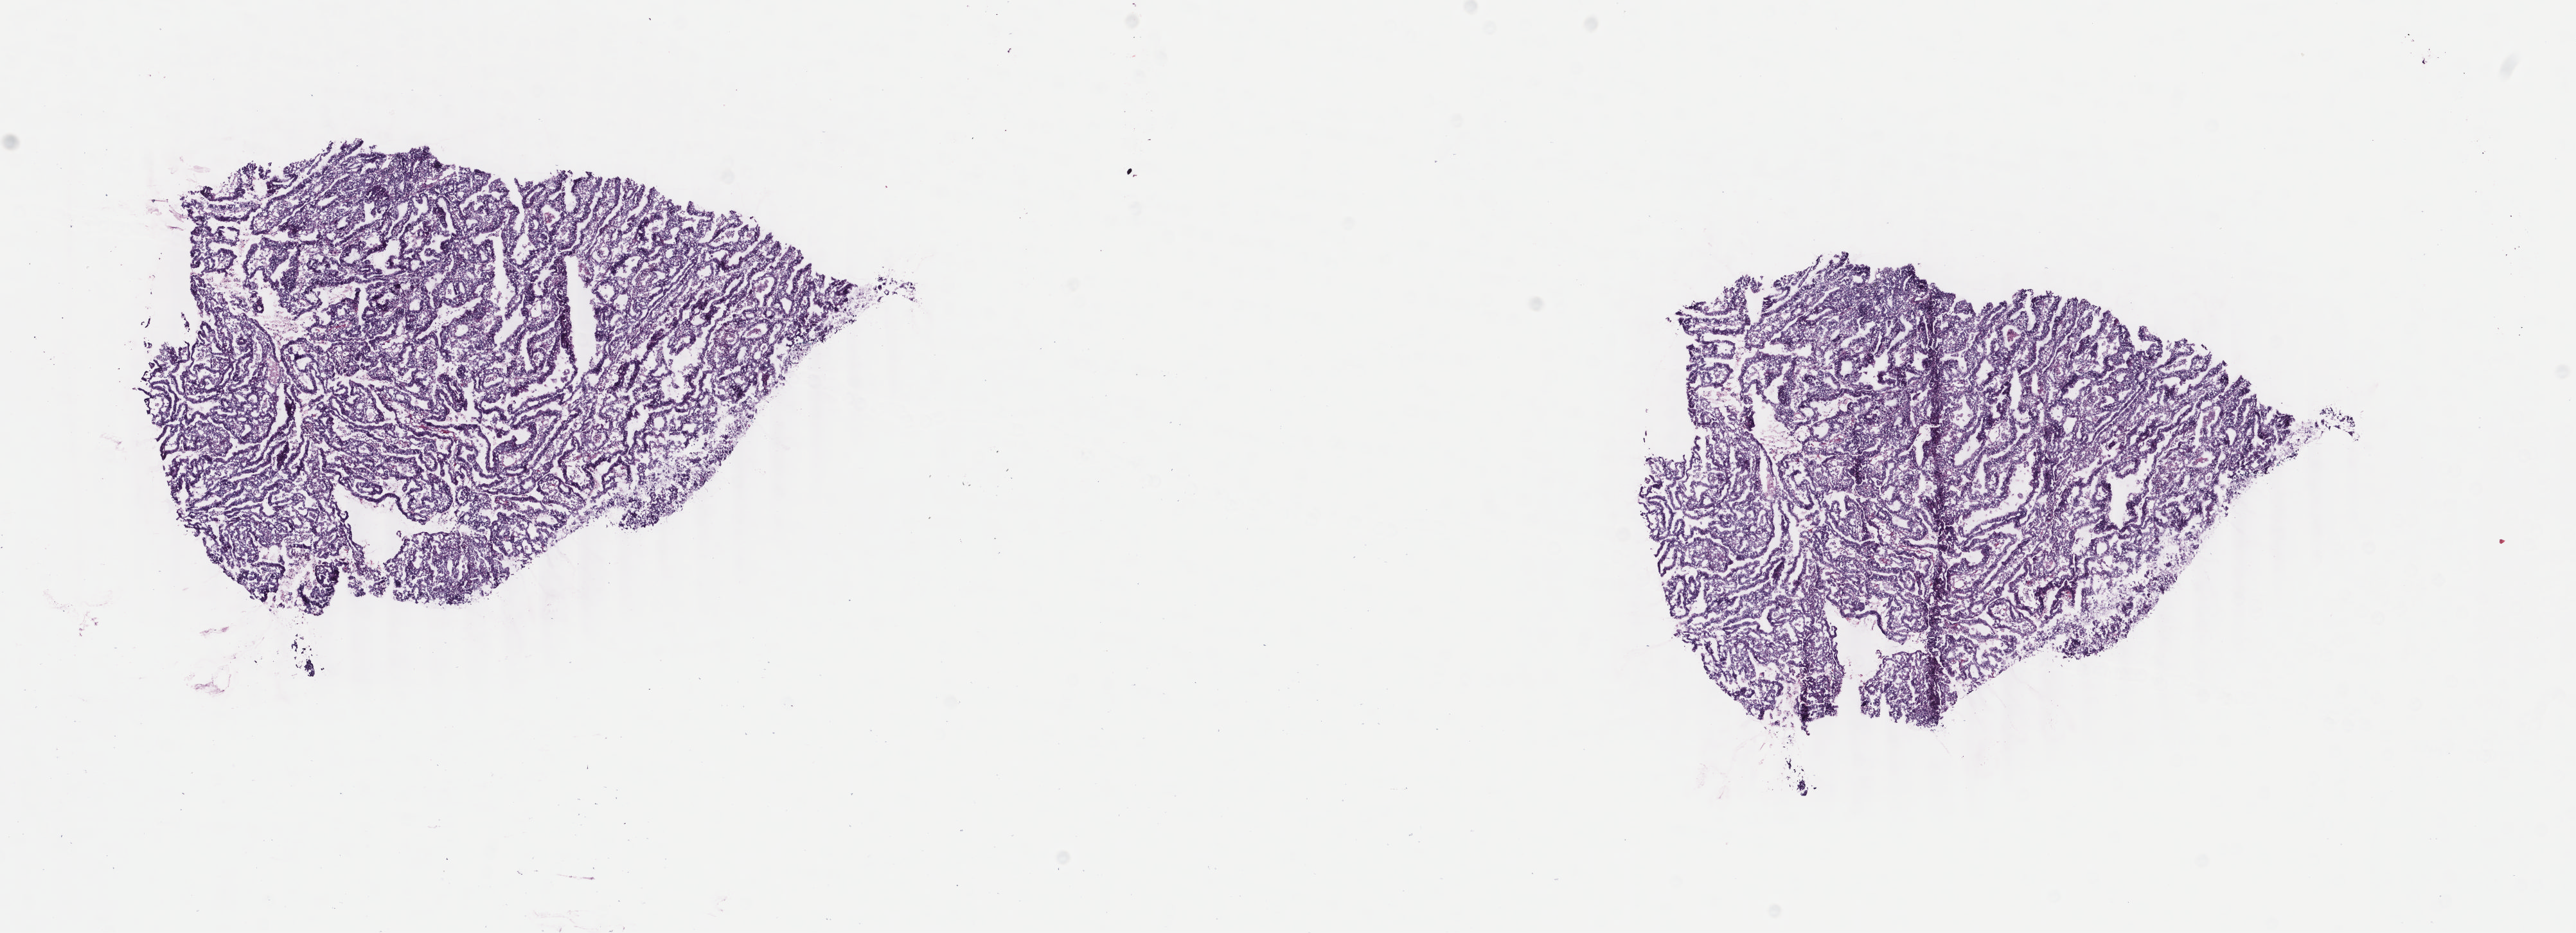
Digitized H&E-stained tissue section (whole slide), low-resolution overview of the scanned area, about 15.9 x 5.8 mm (from a 40x scan), frozen section from the bottom of the tissue portion, primary tumour sample from the uterus. Female, age 65 years at initial diagnosis. Histologic grade: G1 (well differentiated). Slide review estimates, as recorded: tumour cells 80%, tumour nuclei 80%, normal cells 0%, stromal cells 15%, necrosis 5%. Infiltration values recorded for this section: lymphocyte infiltration 40%, monocyte infiltration 20%, neutrophil infiltration 20%.
• pathologic diagnosis: Endometrioid adenocarcinoma, NOS (corpus uteri)
• FIGO stage: IB